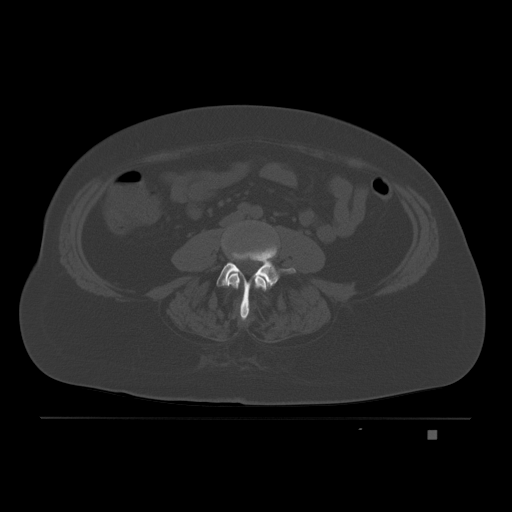
CT including the spine, one axial slice. Position 44 of 221 along the scan axis. Bone window (W 1800 / L 400 HU). 3 mm slice thickness. 512 × 512 image matrix, field of view 474 × 474 mm. Patient: female, 63 years. From the clinical record (not read from this slice): primary cancer: breast.
Annotated regions visible in this slice (semi-automatically segmented with operator editing):
- L3 vertebra: bounding box <222,243,270,291> (left, top, right, bottom; pixels)
- L4 vertebra: <216,245,296,321>